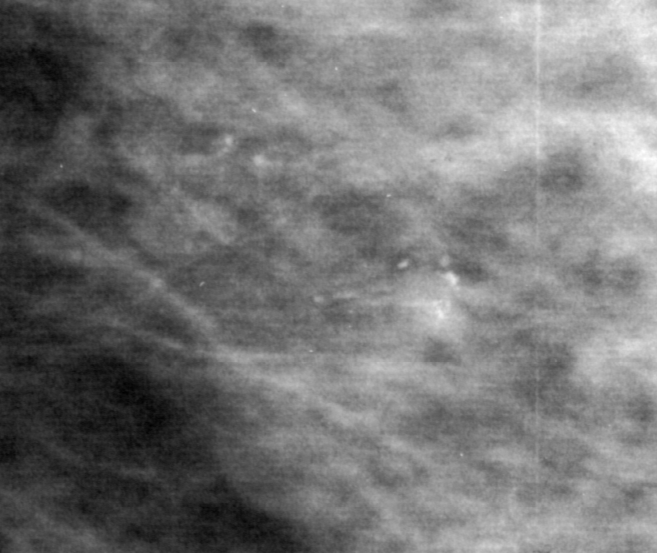
Crop from a digitized film mammogram around one marked abnormality; right breast; MLO view.
Marked abnormality: calcifications, morphology pleomorphic, distribution segmental; BI-RADS assessment category 4; pathology (as recorded): benign.